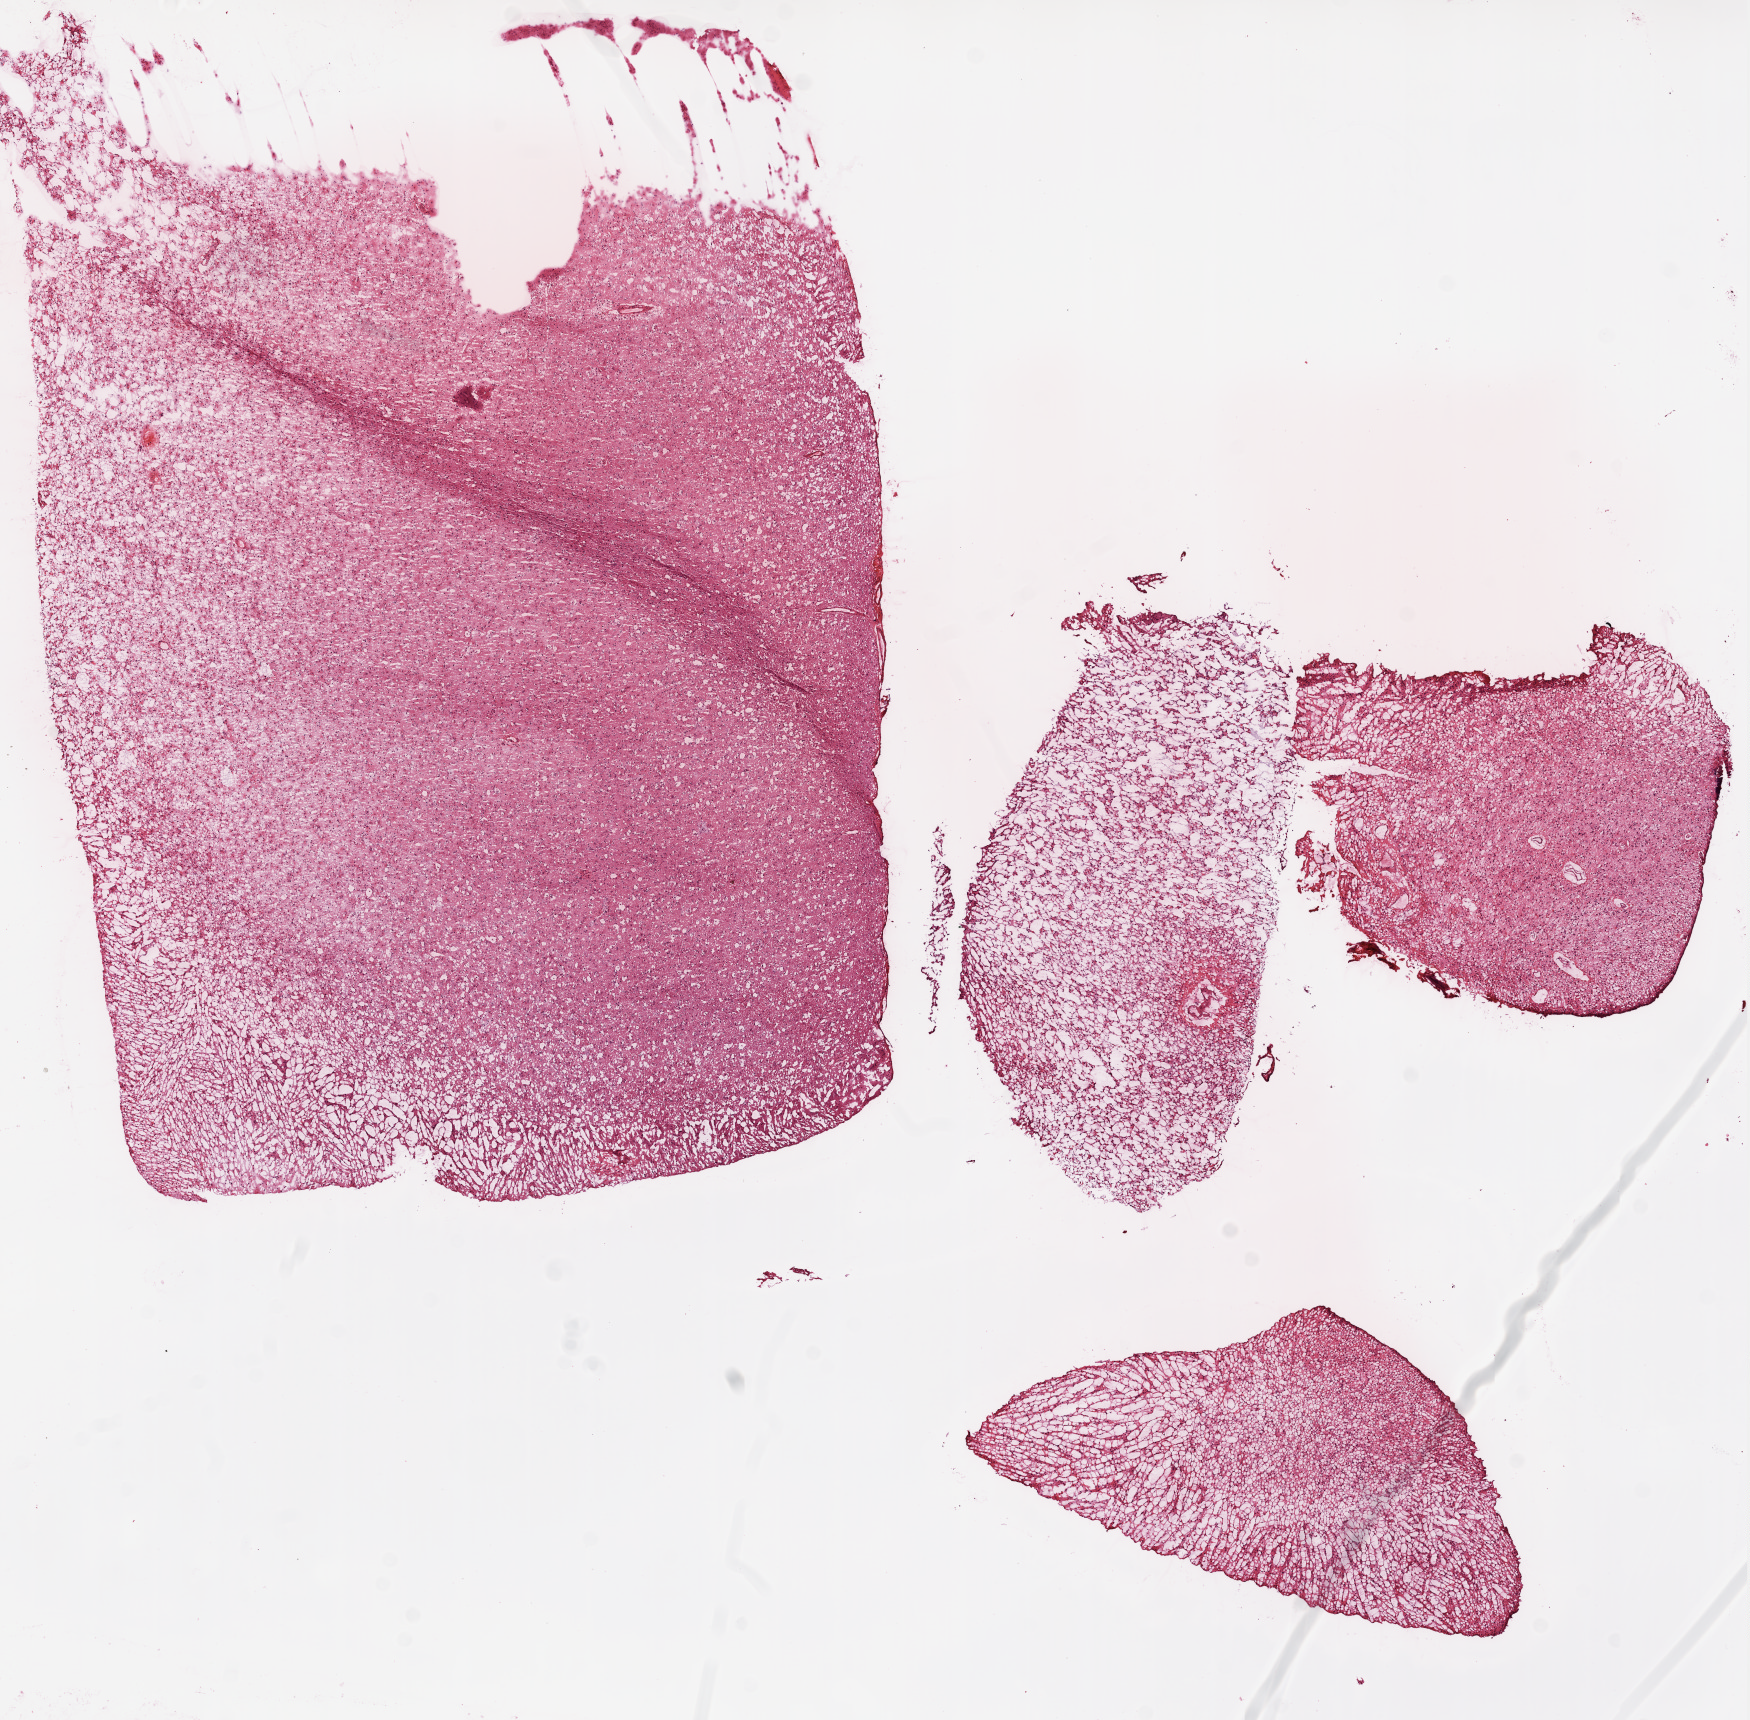
Whole-slide histology image, Hematoxylin and eosin (H&E) stained, shown as a low-resolution overview of the whole scanned area (about 14.0 x 13.8 mm); frozen section from the top of the tissue portion; sample: primary tumour, brain. Female, age 62 years at initial diagnosis. Histologic grade: G3 (poorly differentiated). Pathologist review of this section (percent, as recorded): tumour cells 100%, tumour nuclei 65%, normal cells 0%, stromal cells 0%, necrosis 0%.
Diagnosis: Astrocytoma, anaplastic.